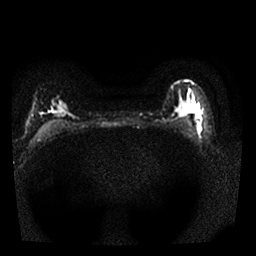
Breast MRI, one axial slice. Slice 18 of 25 in the series (ordered by position). Diffusion-weighted series; image 2 of 4 stored at this slice position (different b-values; order by instance number). 1.5 T. 4 mm slice thickness. 256 × 256 image matrix. Female patient.
Annotated regions visible in this slice (outlined manually by an expert reader):
- tumour on diffusion-weighted imaging: box from (x=198, y=126) to (x=201, y=131) px